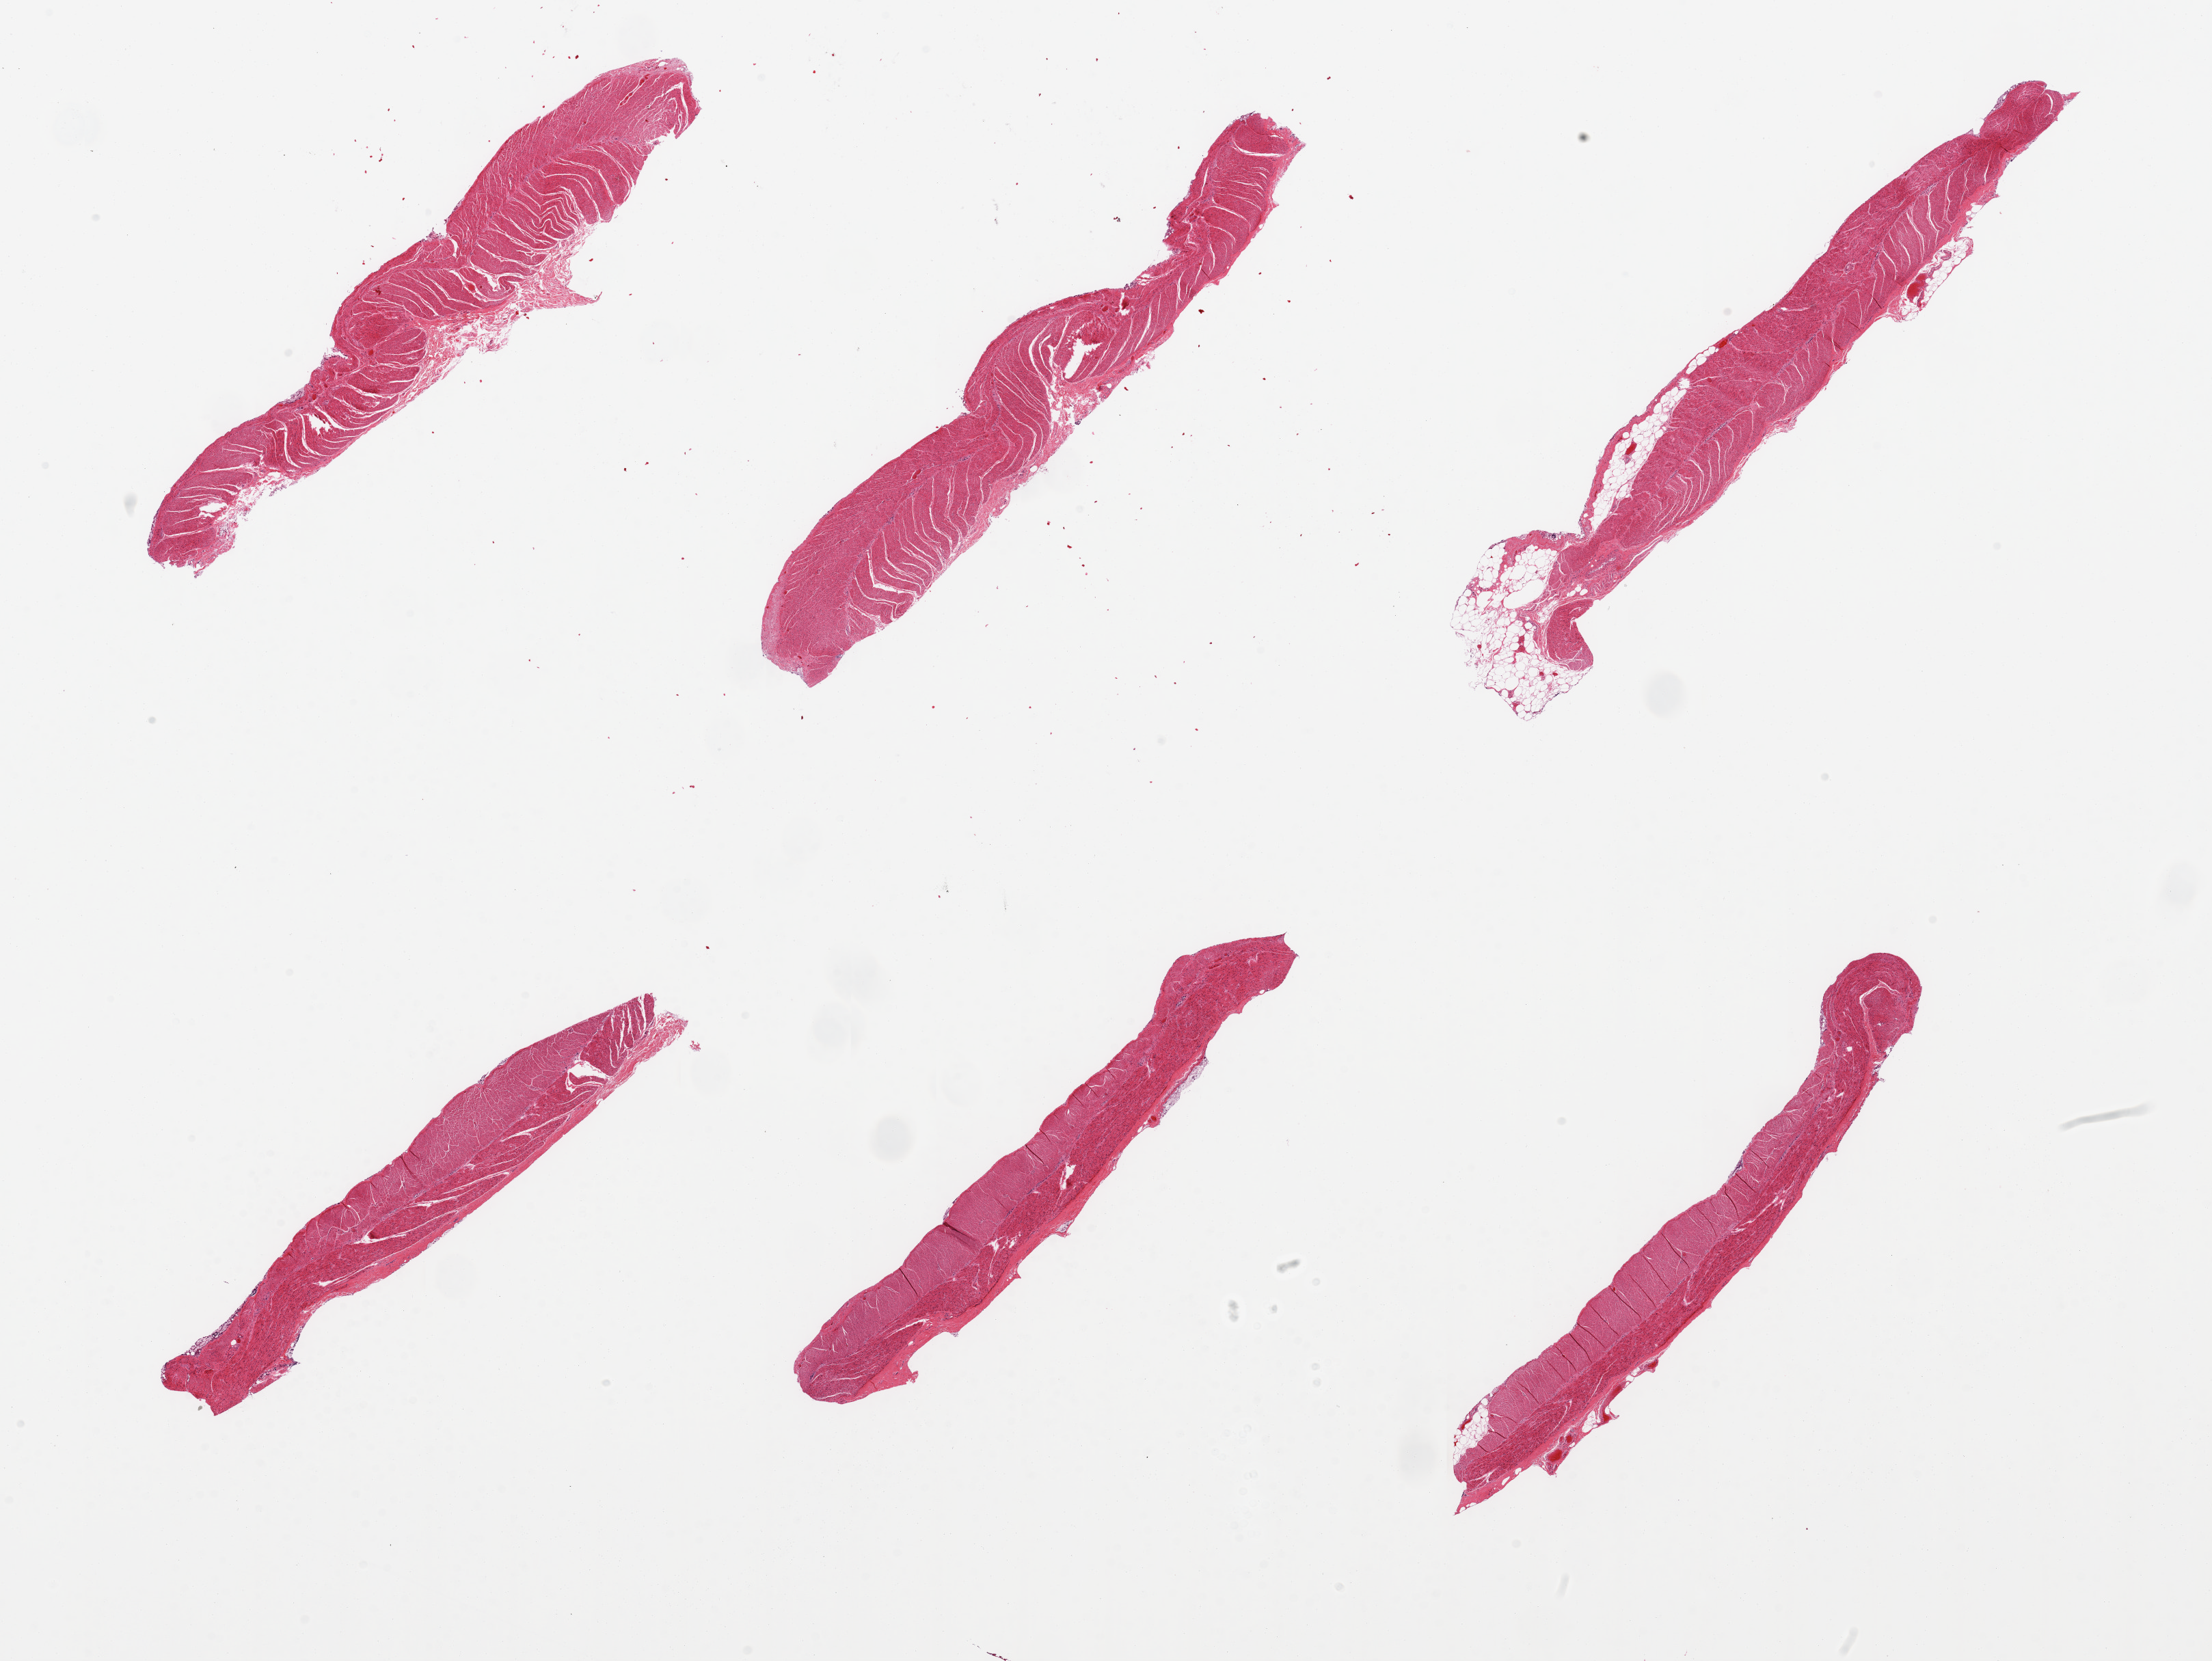
Digitized hematoxylin and eosin (H&E)-stained section, brightfield — a low-resolution overview of the entire scanned area, about 25.6 x 19.2 mm. PAXgene-fixed paraffin-embedded (PFPE) section. Sampled site (target tissue): sigmoid colon. Donor tissue sample. Male donor.
Reviewer comment on this tissue sample: 6 pieces, all muscularis.